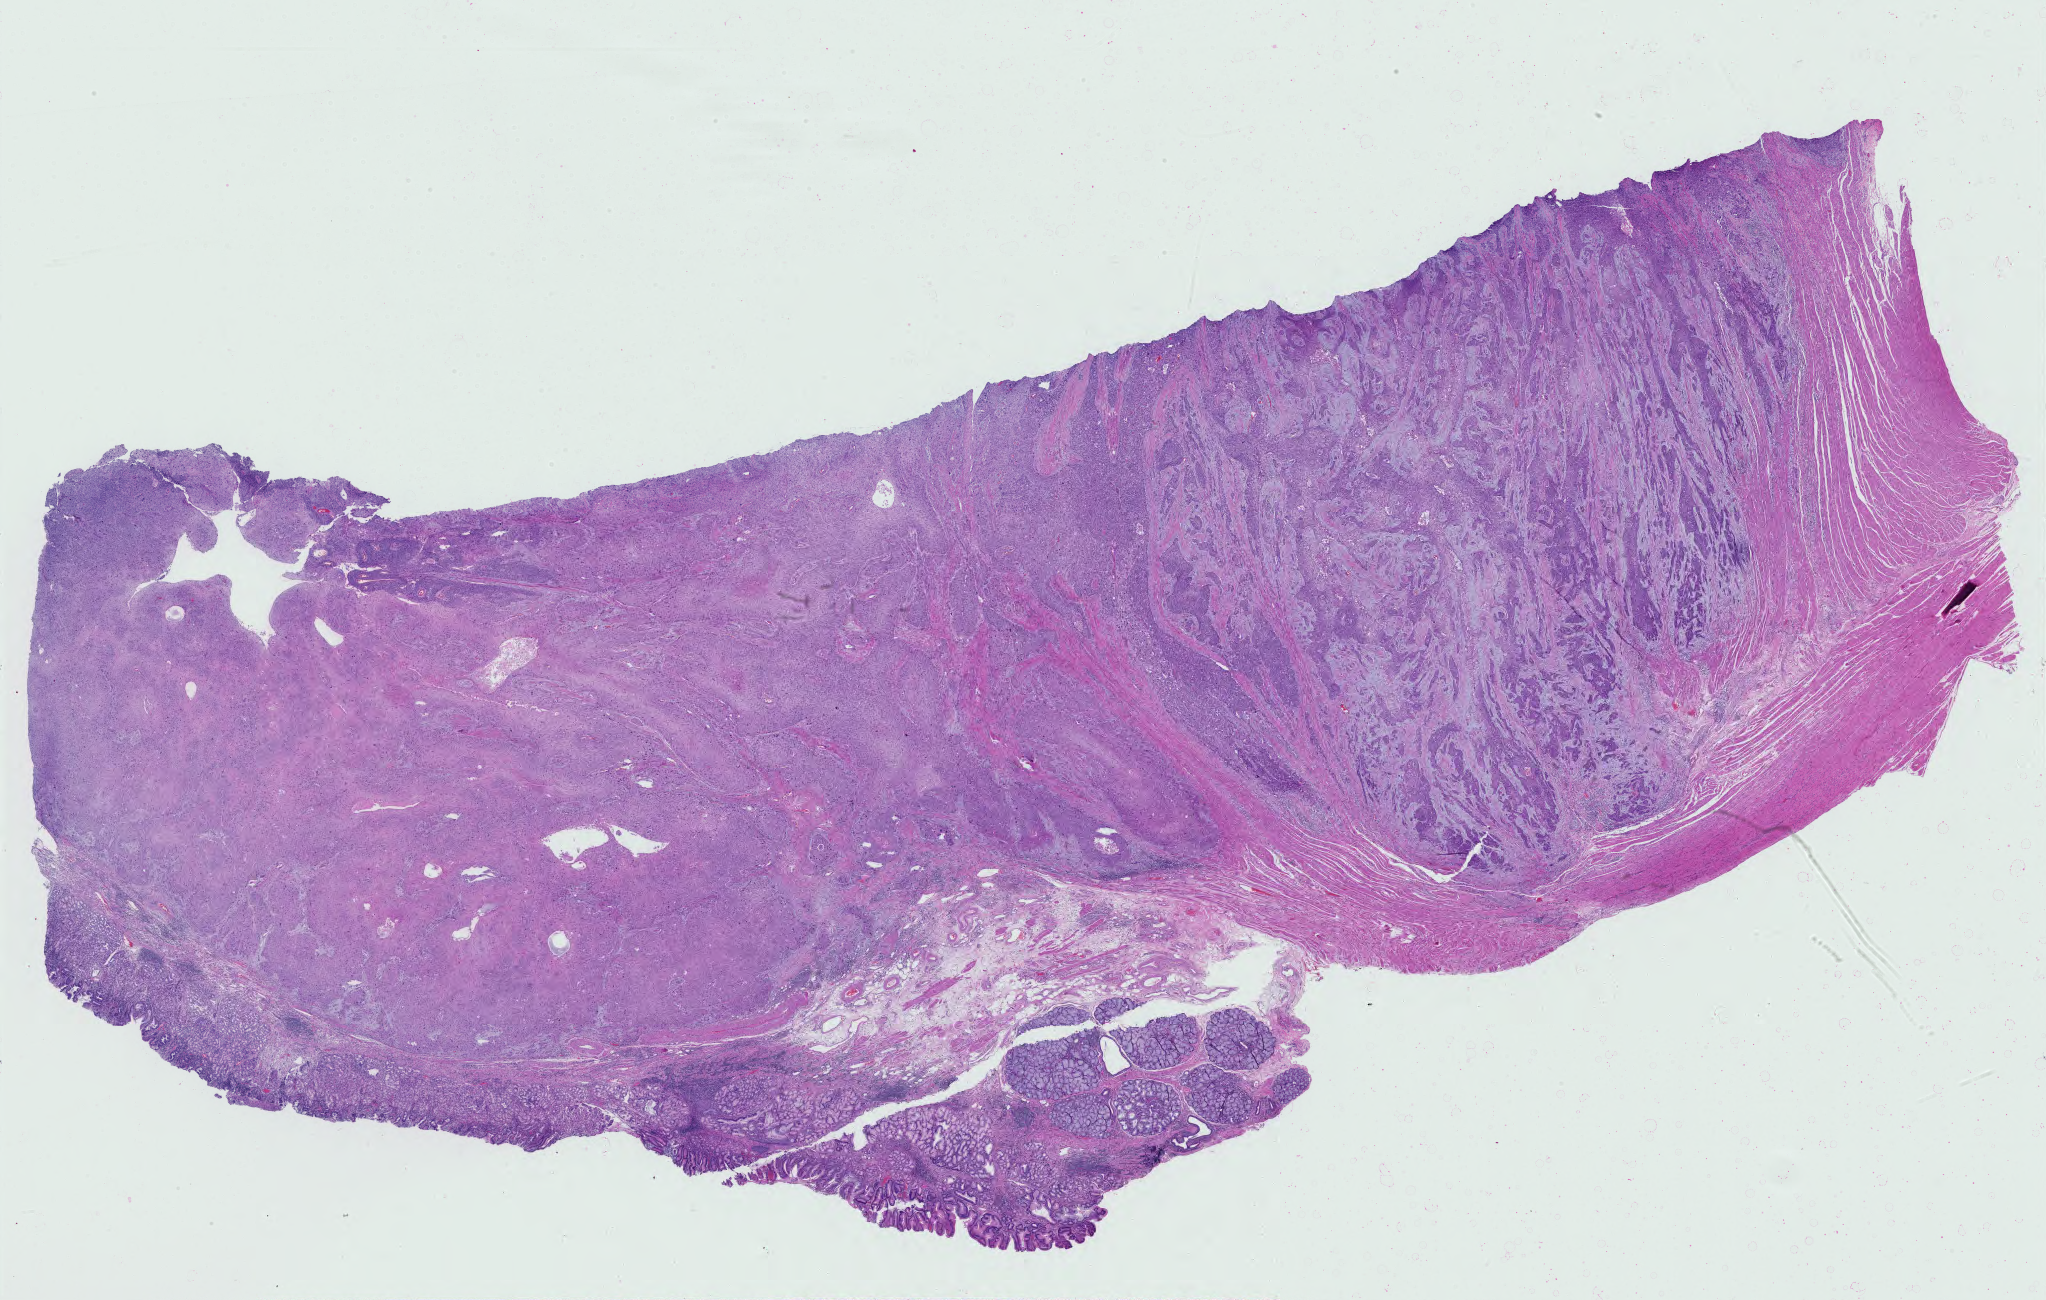
Whole-slide histology image, Hematoxylin and eosin (H&E) stained — low-resolution overview of the scanned area, about 29.7 x 18.9 mm (acquisition: 40x scan), FFPE section, sample: primary tumour, esophagus. Female, age 57 years at initial diagnosis. Histologic grade: G2 (moderately differentiated).
AJCC pathologic stage: IIIB (7th edition). Pathologic diagnosis: Squamous cell carcinoma, NOS (lower third of esophagus).